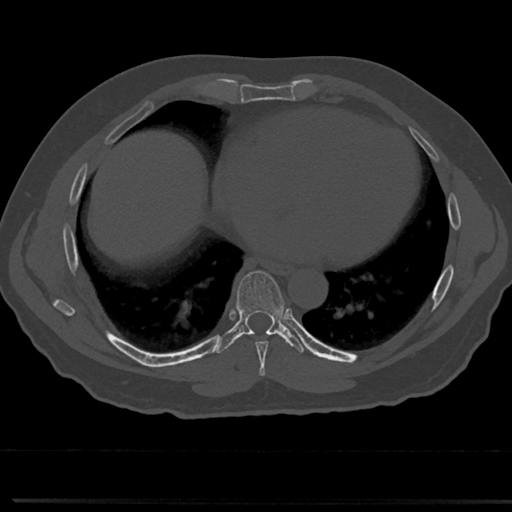
CT including the spine, one axial slice. Slice 371 of 817 in the series (ordered by position). Reconstruction kernel Br40s/3. Bone window (W 1800 / L 400 HU). 512 × 512 image matrix, field of view 355 × 355 mm. Male patient, age 61 years. Case-level facts recorded for this patient, not image findings: primary cancer: prostate.
Annotated regions visible in this slice (semi-automatic segmentation, software-assisted and operator-edited):
- T7 vertebra: bounding box [x1, y1, x2, y2] px = [235, 271, 287, 358]
- T8 vertebra: [237, 325, 282, 334]